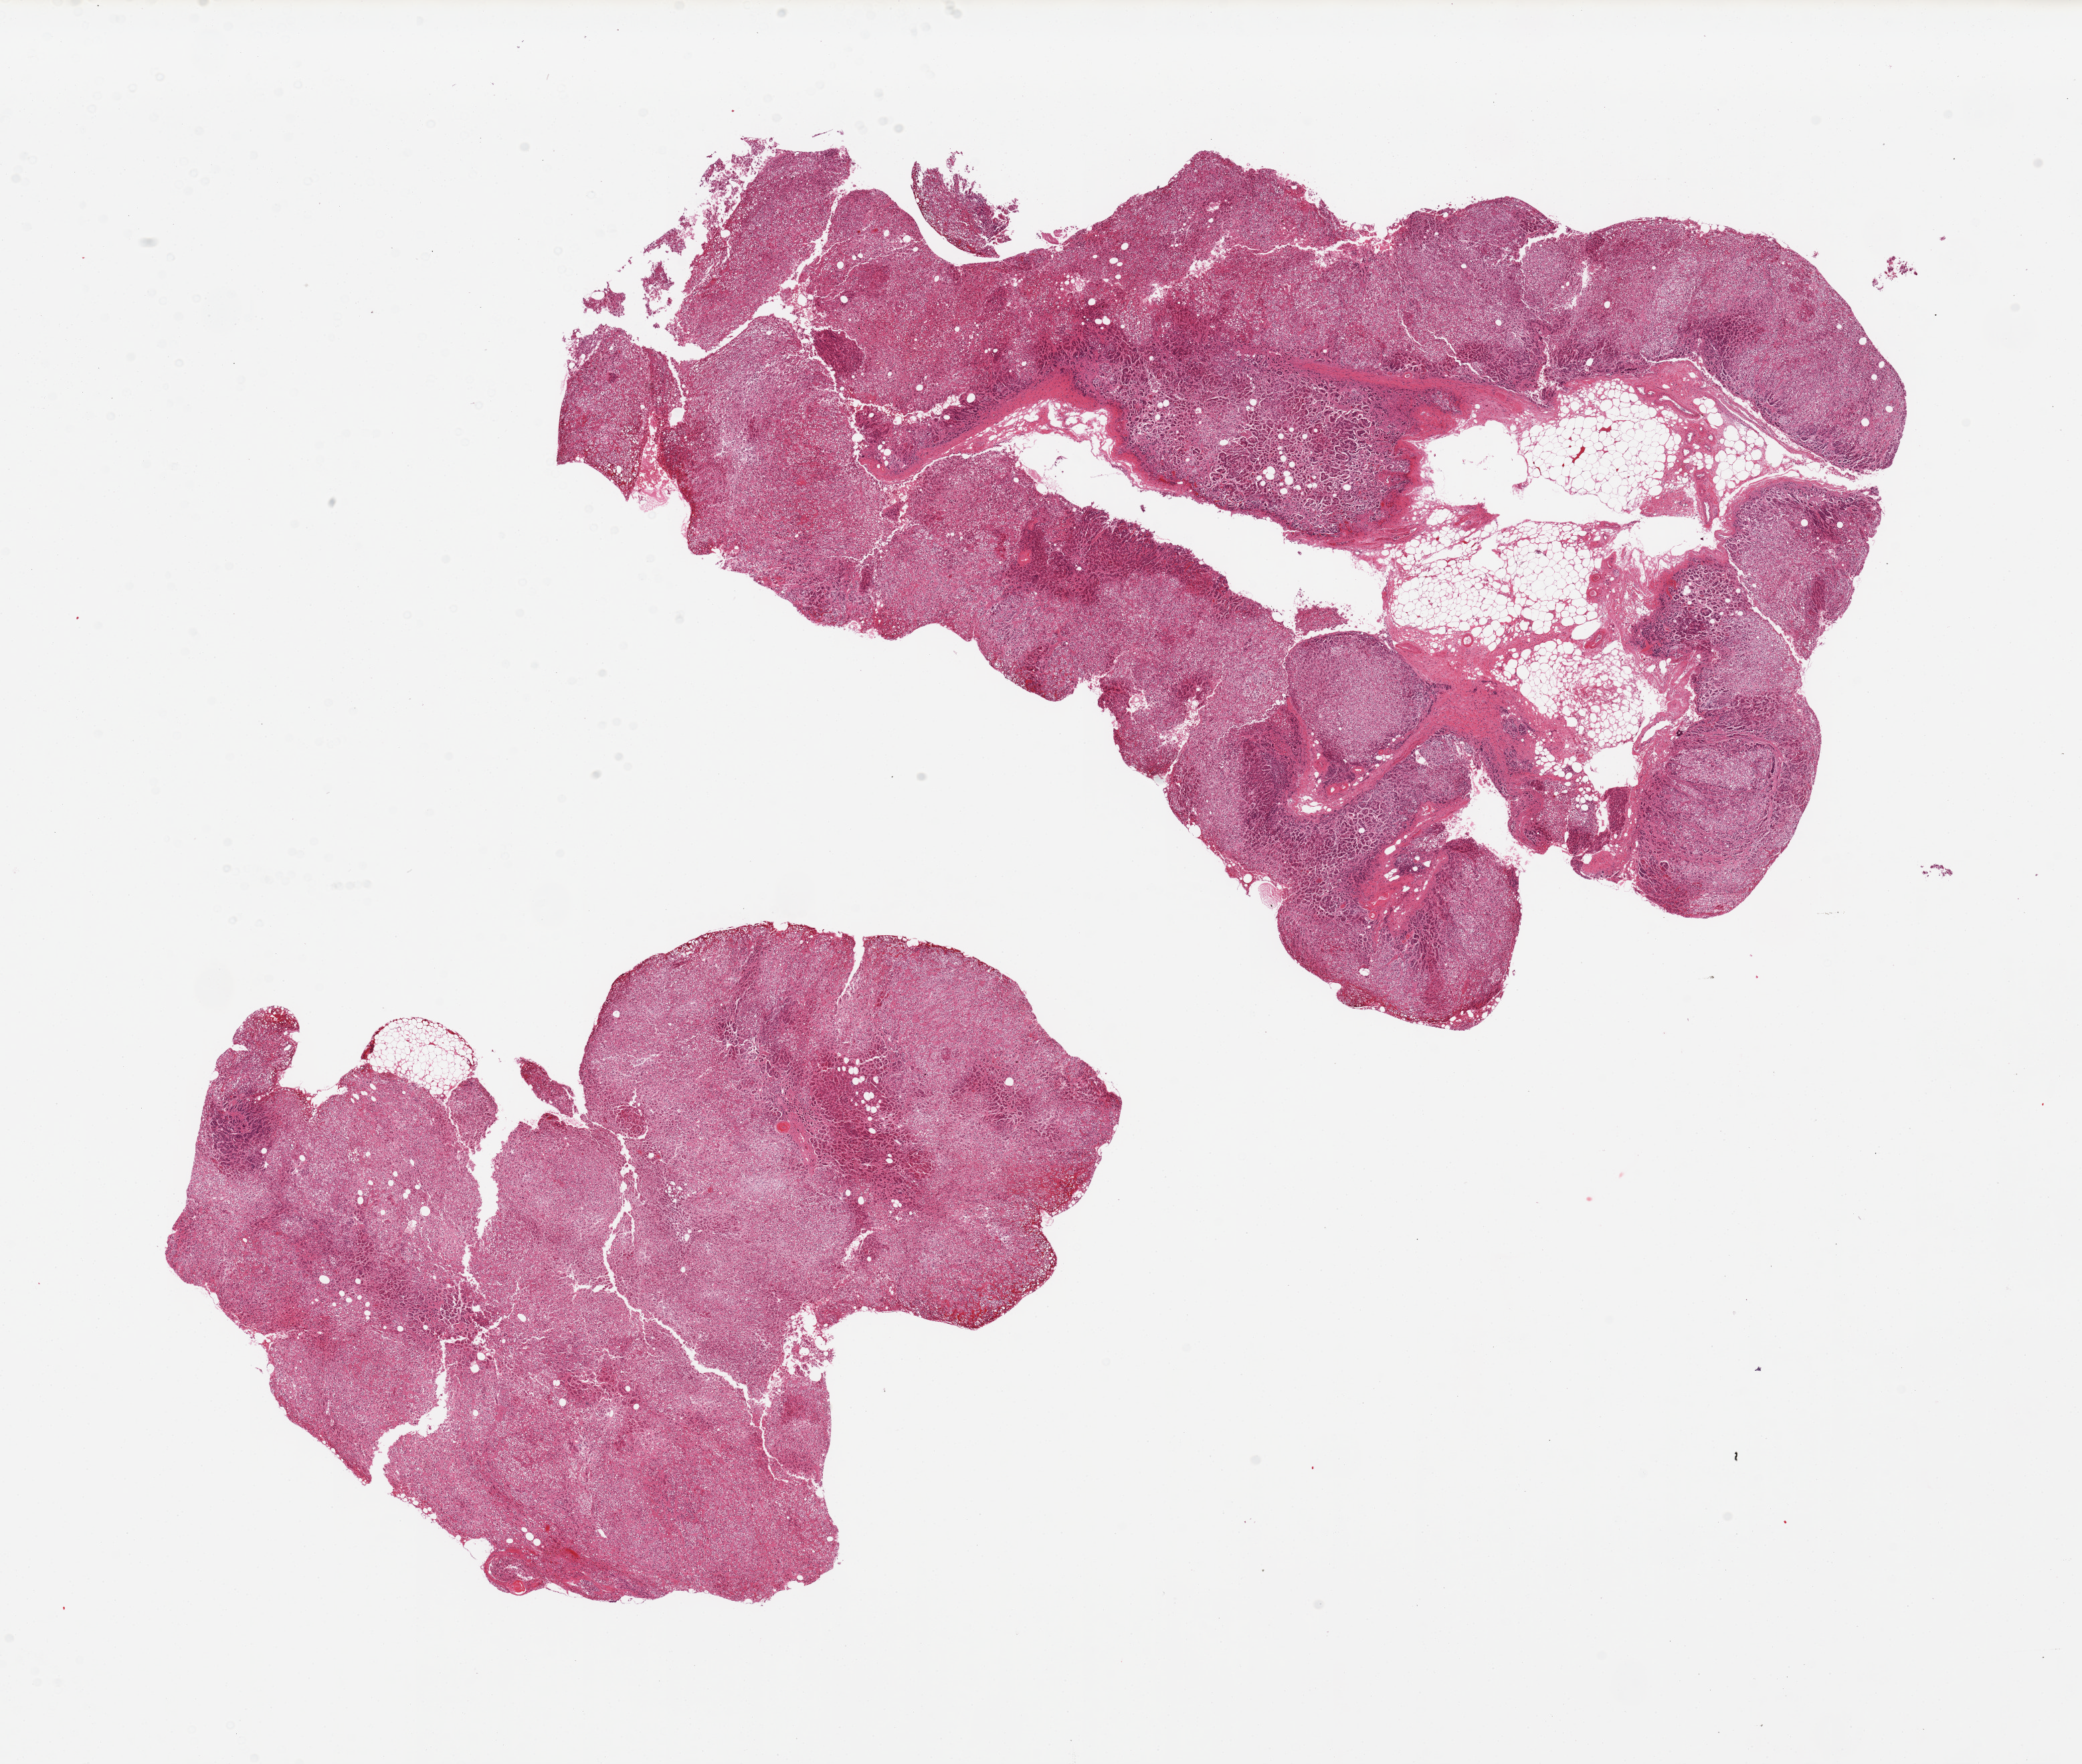
Digitized haematoxylin and eosin-stained section — whole scanned area (about 24.6 x 20.9 mm, acquisition: 20x scan) shown as a low-resolution overview; PAXgene-fixed paraffin-embedded (PFPE) section; sampled site (target tissue): adrenal gland; donor tissue sample. Male donor.
* pathologist's review note for this sample: 2 pieces, one piece is ~10% fat